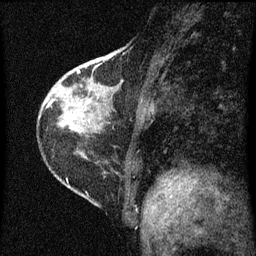
Breast MRI (dynamic contrast-enhanced), one sagittal slice; slice 21 of 60 in the series (ordered by position); dynamic contrast-enhanced series, image 2 of 3 at this slice position (ordered by acquisition); 1.5 T; TE 4.2 ms, TR 8 ms; 2 mm slice thickness; 256 × 256 image matrix. Female patient, age 38 years.
Structures marked on this image (semi-automatic segmentation, software-assisted and operator-edited):
- analysis volume of interest (the breast-tissue region the enhancement analysis was run in; not a lesion): box from (x=67, y=46) to (x=138, y=131) px
- tumour enhancement mask (voxels above the 70 % enhancement threshold inside the analysis volume of interest): (x=77, y=70)–(x=80, y=73)